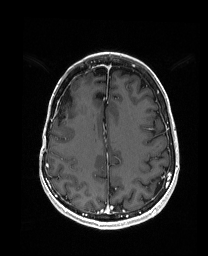
Brain MRI from a brain-tumour surgery series, one axial slice. Position 61 of 192 along the scan axis. T1-weighted post-contrast. 208 × 256 image matrix, field of view 203 × 250 mm. Case-level facts recorded for this patient, not image findings: histopathology: Metastatic Carcinoma from Breast primary; tumour location: Right Frontal.
Annotated regions visible in this slice (expert manual segmentation):
- previous resection cavity: box from (x=61, y=84) to (x=71, y=105) px